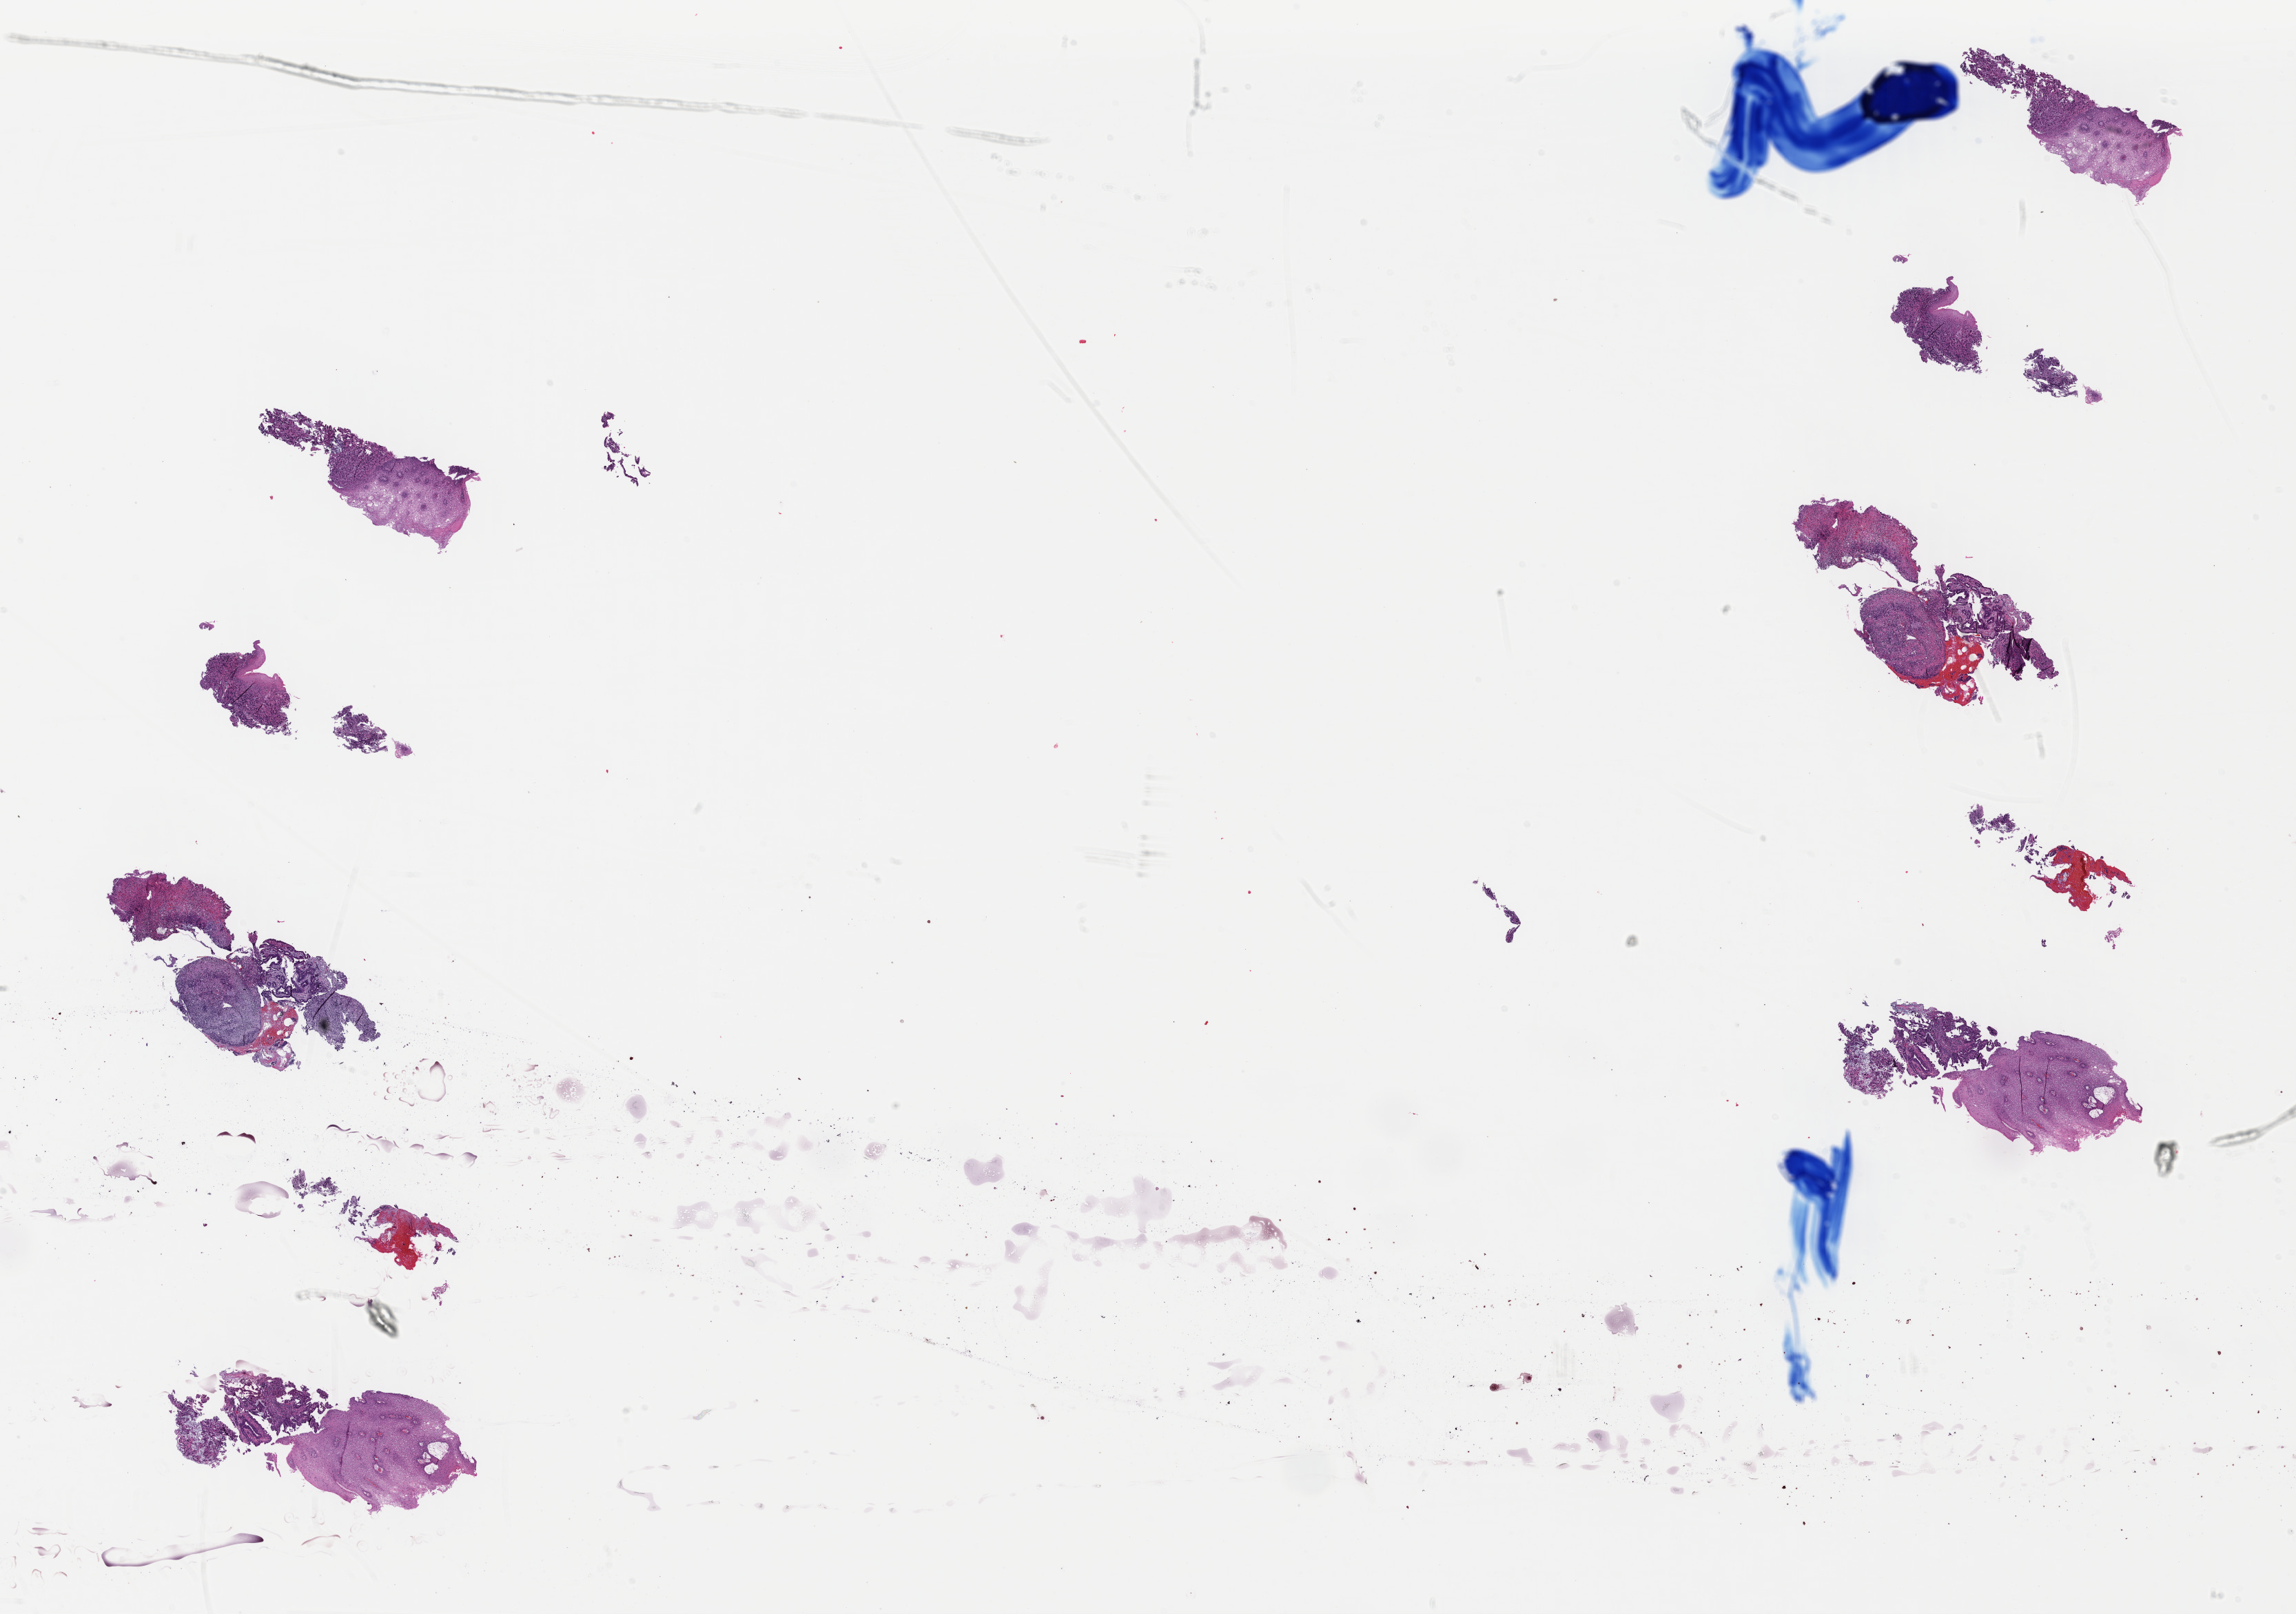
H&E whole-slide image, shown as a low-resolution overview of the whole scanned area (about 26.2 x 18.4 mm, acquisition: 40x scan); FFPE section; primary tumour sample from the esophagus. Patient: male, age at initial diagnosis 42 years. Histologic grade: G3 (poorly differentiated). Pathologist review of this section (percent, as recorded): tumour cells 60%, tumour nuclei 75%, normal cells 25%, stromal cells 10%, necrosis 5%. Inflammatory infiltration, as recorded: lymphocyte infiltration 2%, monocyte infiltration 2%, neutrophil infiltration 2%.
Diagnosis: Adenocarcinoma, NOS.